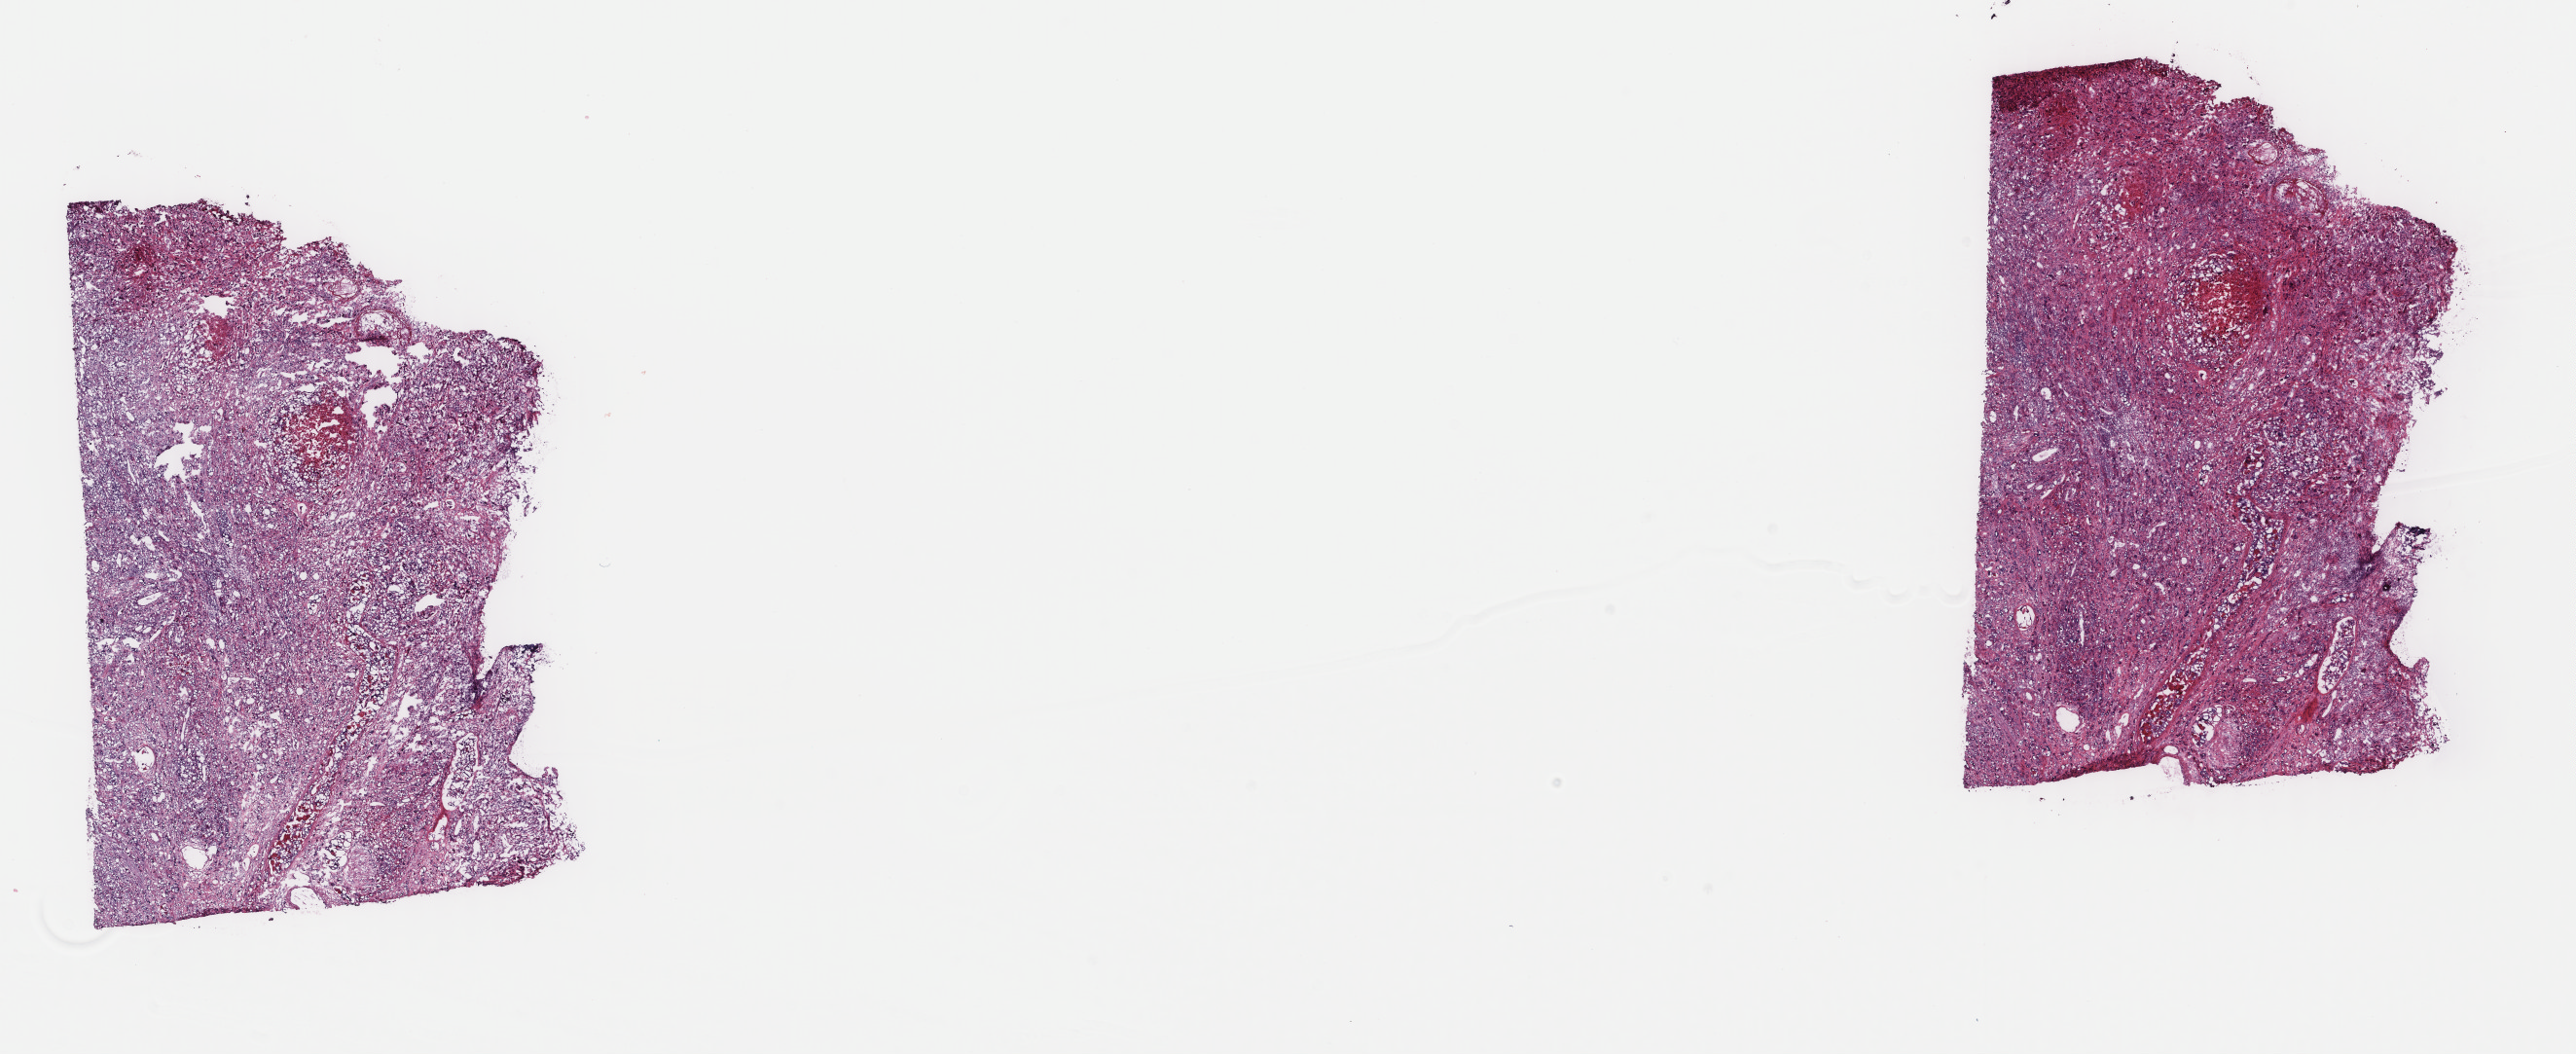
Digitized H&E-stained tissue section (whole slide) — low-resolution overview of the scanned area, about 21.0 x 8.6 mm (slide scanned at 40x). Frozen section from the top of the tissue portion. Bladder, primary tumour sample. Patient: female, age at initial diagnosis 78 years. Histologic grade: high grade. Composition of this section per pathologist review: tumour cells 85%, tumour nuclei 90%, normal cells 0%, stromal cells 15%, necrosis 0%. Inflammatory infiltration, as recorded: lymphocyte infiltration 0%, monocyte infiltration 0%, neutrophil infiltration 0%.
* histologic diagnosis: Transitional cell carcinoma (trigone of bladder)
* lymph nodes positive (case pathology): 1 of 16 examined
* AJCC pathologic stage: IV